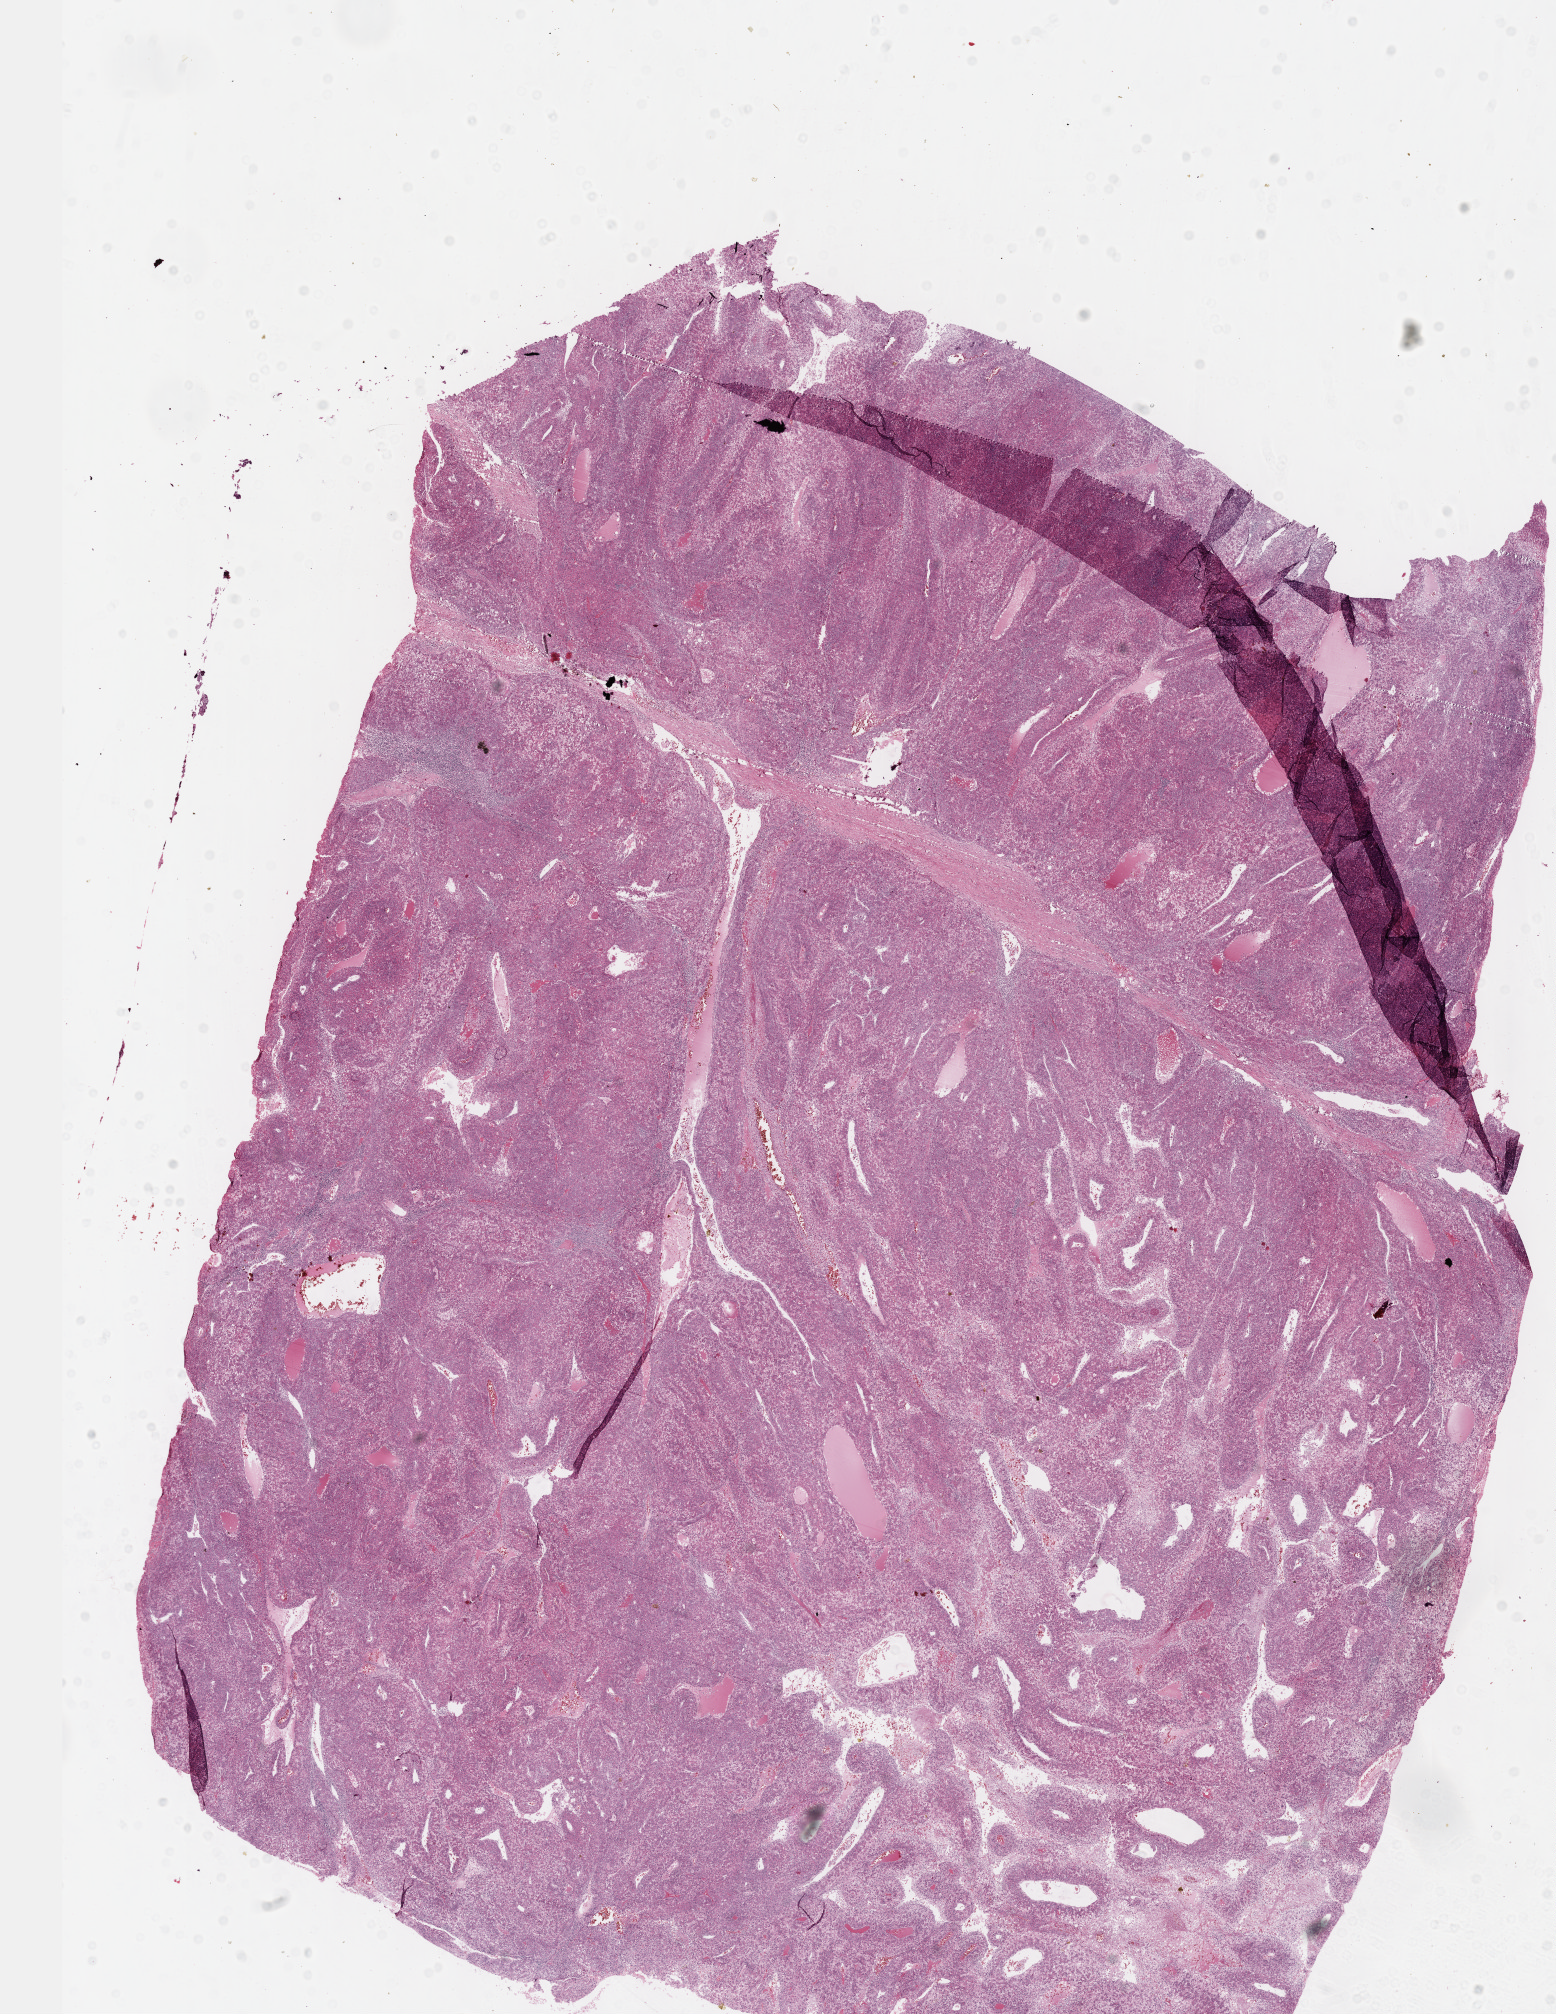
H&E-stained whole-slide image — a low-resolution overview of the entire scanned area, about 12.6 x 16.3 mm, formalin-fixed paraffin-embedded (FFPE) diagnostic section, primary tumour sample from the liver. Male, age 68 years at initial diagnosis.
Diagnosis: Hepatocellular carcinoma, NOS.